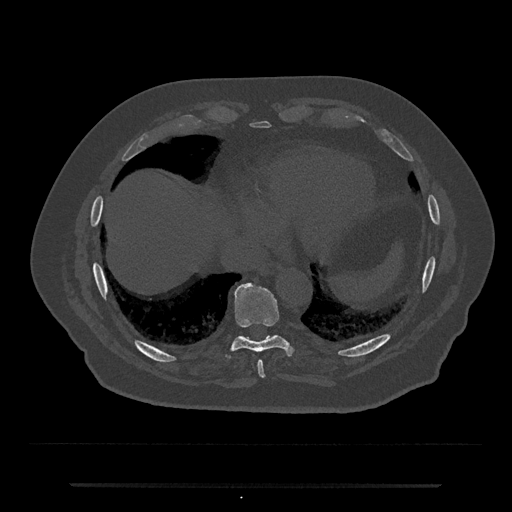
CT including the spine, one axial slice. Slice 755 of 797 in the series (ordered by position). 120 kVp. Bone window (W 1800 / L 400 HU). 0.5 mm slice thickness. 512 × 512 image matrix, field of view 434 × 434 mm. Male patient, age 80 years. From the clinical record (not read from this slice): primary cancer: prostate; vertebrae with lytic lesions (as recorded): L1, T11.
Structures marked on this image (semi-automatic segmentation, software-assisted and operator-edited):
- T8 vertebra: box from (x=257, y=361) to (x=265, y=378) px
- T9 vertebra: (x=232, y=282)–(x=291, y=355)